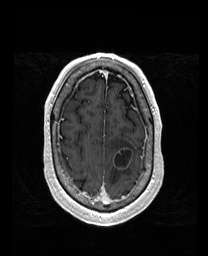
Brain MRI from a brain-tumour surgery series, one axial slice. Slice 144 of 192 in the series (ordered by position). T1-weighted post-contrast. 1 mm slice thickness. 208 × 256 image matrix. Case-level facts recorded for this patient, not image findings: histopathology: Metastatic Carcinoma from Lung Adenocarcinoma; tumour location: Left Frontal.
Structures marked on this image (manually delineated by an expert):
- tumour: box from (x=113, y=149) to (x=133, y=170) px